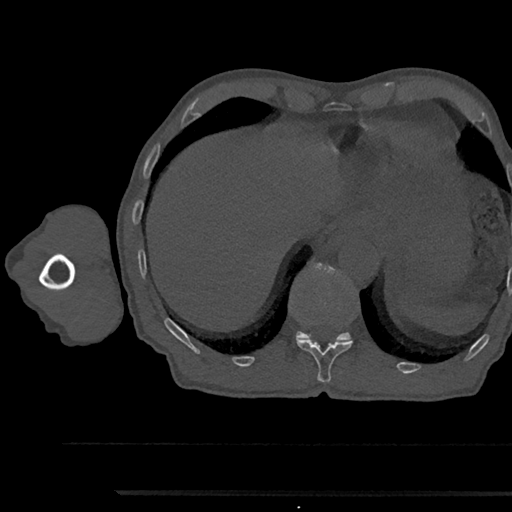
CT including the spine, one axial slice. Position 761 of 797 along the scan axis. Reconstruction kernel Br40s/3. 120 kVp. Bone window (W 1800 / L 400 HU). 0.5 mm slice thickness. 512 × 512 image matrix, field of view 367 × 367 mm. Patient: male, 79 years. From the clinical record (not read from this slice): primary cancer: prostate.
Outlined on this slice (semi-automatically segmented with operator editing):
- T11 vertebra: box from (x=296, y=338) to (x=352, y=383) px
- T12 vertebra: (x=296, y=264)–(x=352, y=342)